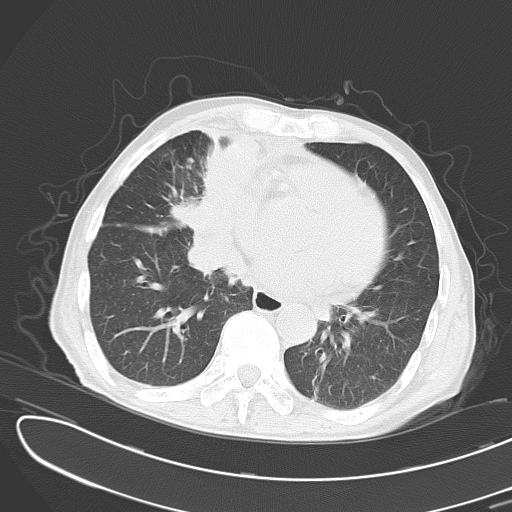
Chest CT, one axial slice. Position 11 of 43 along the scan axis. Reconstruction kernel B70f. Lung window (W 1500 / L -600 HU). 5 mm slice thickness. 512 × 512 image matrix, field of view 353 × 353 mm. Male patient, age 65 years. From the clinical record (not read from this slice): clinical TNM (as recorded): T2 N3 M1.
Structures marked on this image (rectangle marked by the reading radiologist):
- lung tumour (recorded histology: small cell carcinoma): bounding box (x1, y1, x2, y2) in pixels: (169, 109, 263, 286)